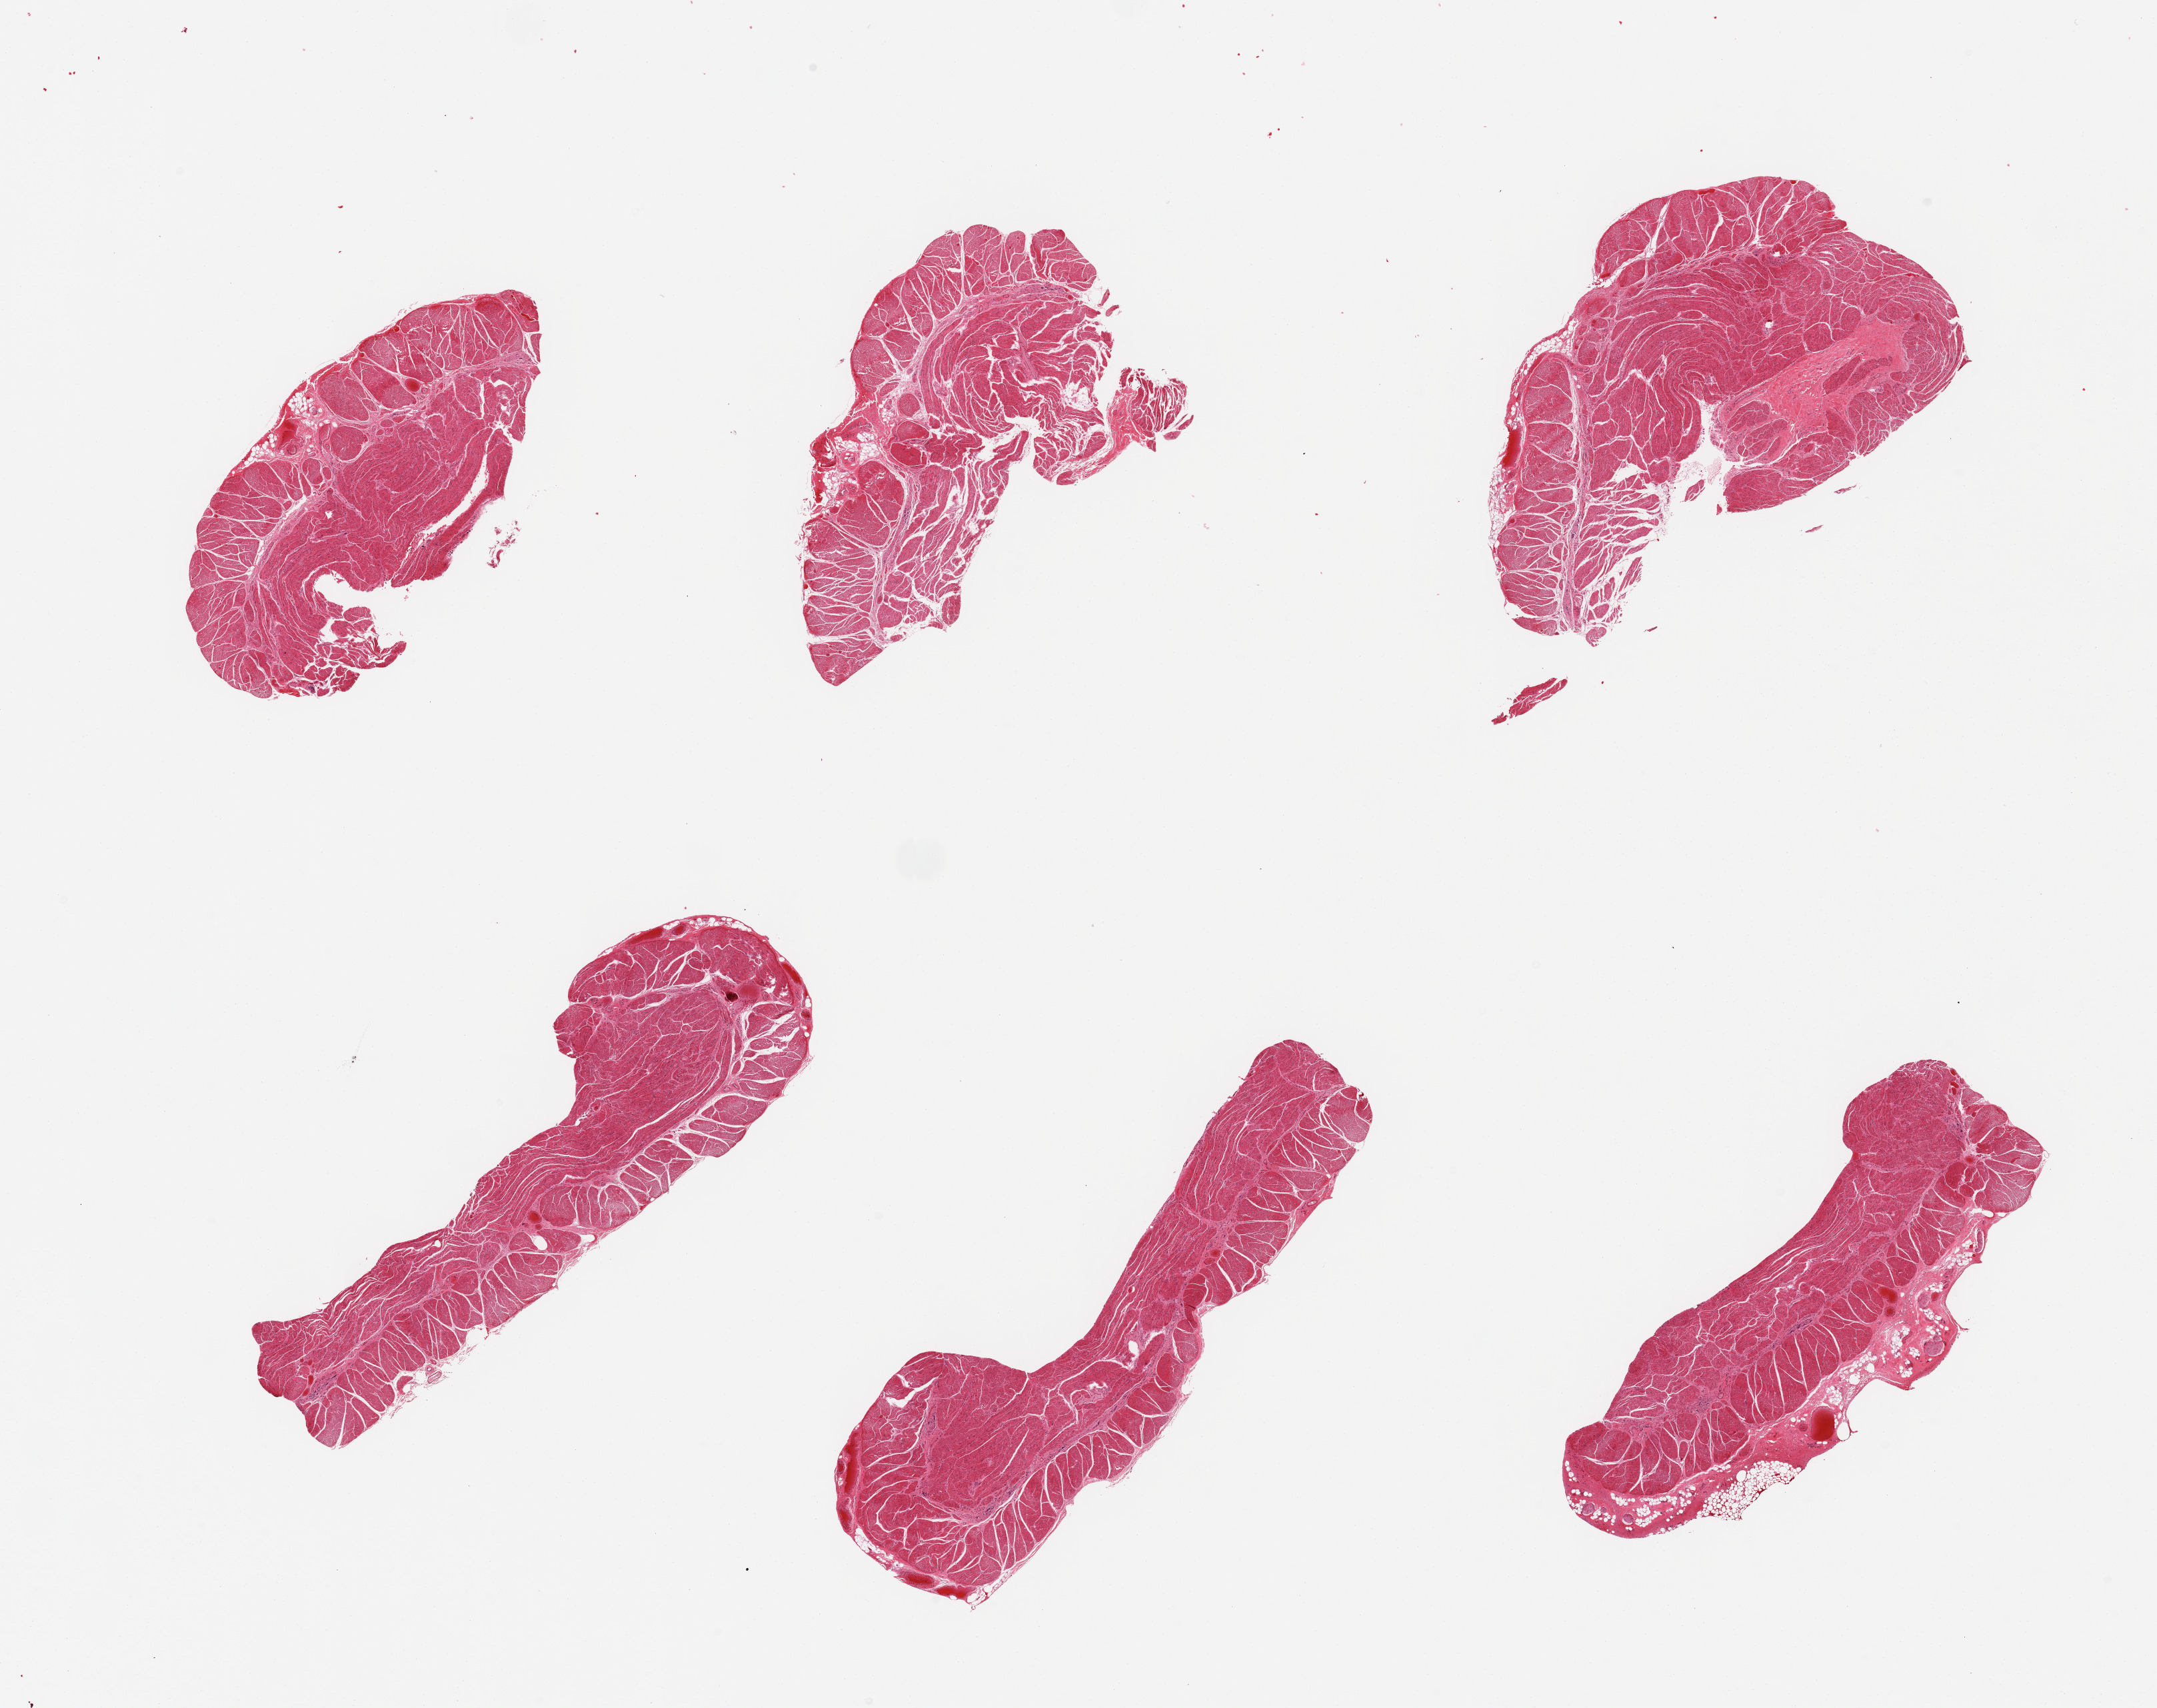
Haematoxylin and eosin whole-slide image — low-resolution overview of the scanned area, about 25.6 x 20.3 mm. PAXgene-fixed, paraffin-embedded tissue. Sampled site (target tissue): esophageal muscle. Donor tissue sample.
* reviewer comment on this tissue sample: 6 pieces; well trimmed muscle